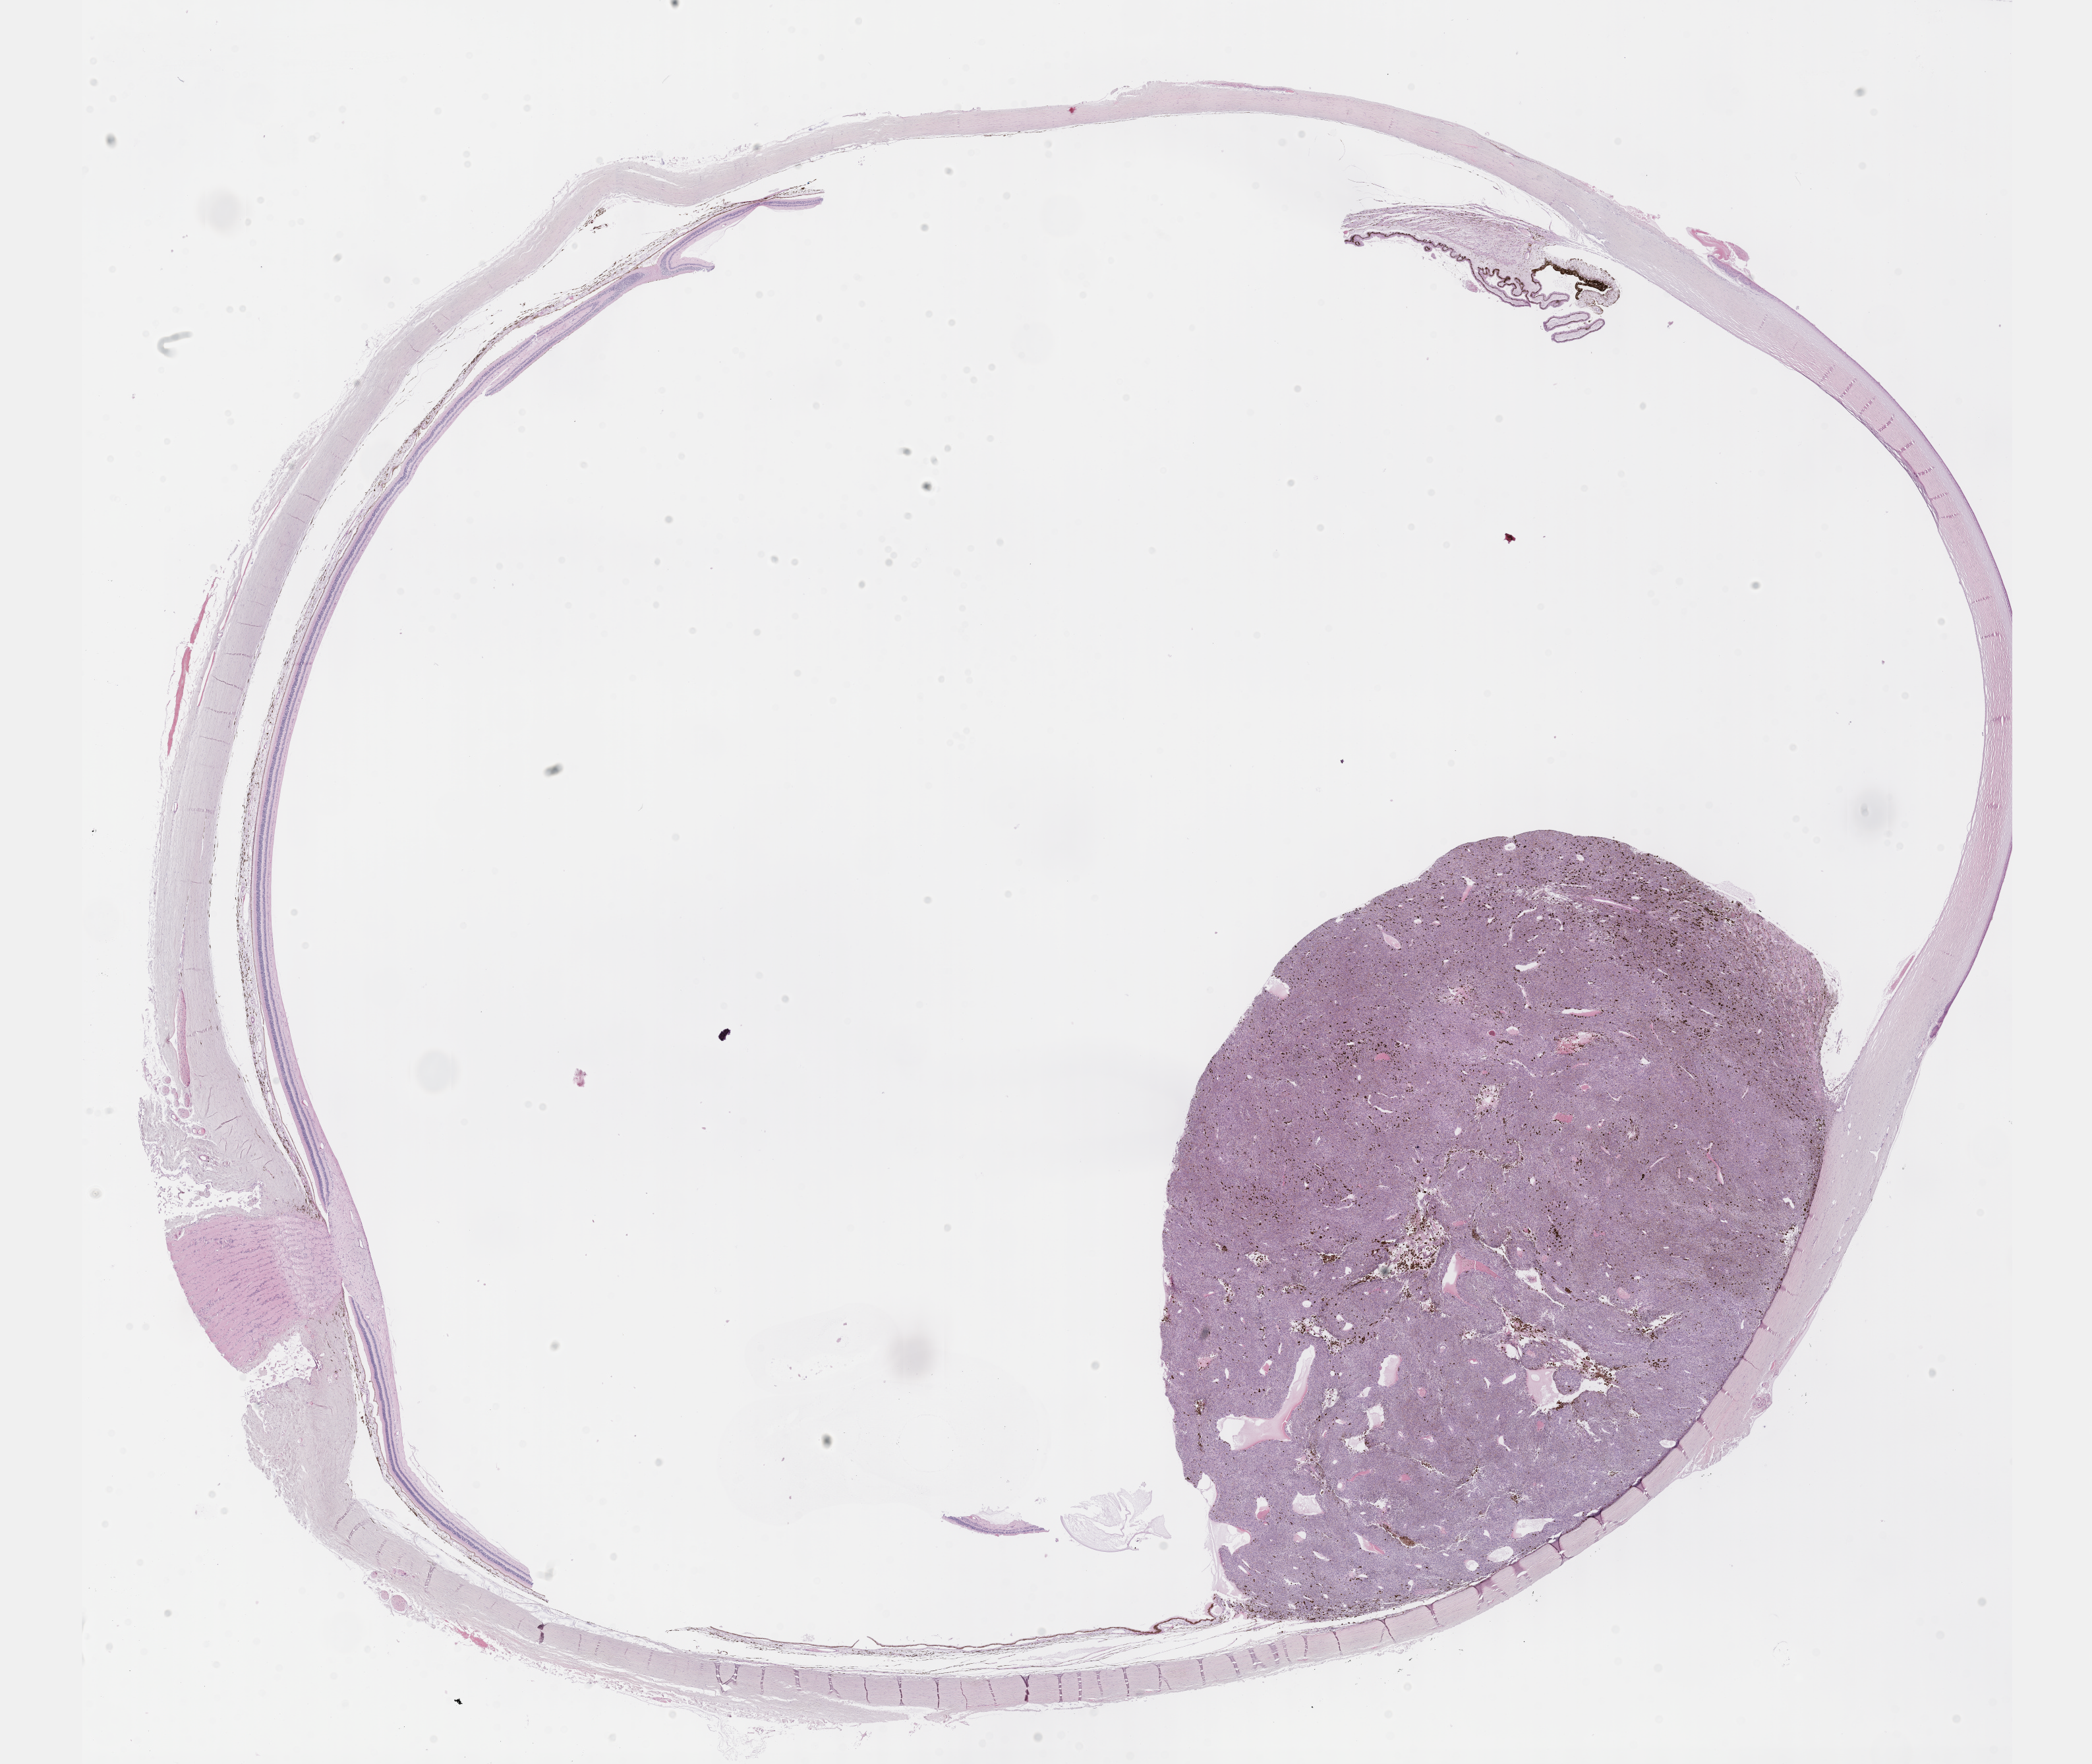
Whole-slide histology image, H&E — whole scanned area (about 25.7 x 21.6 mm, from a 40x scan) shown as a low-resolution overview; FFPE section; sample: primary tumour, uvea. Female patient; age at initial diagnosis 51 years.
TNM: T4b N0 M0. Diagnosis: Malignant melanoma, NOS. AJCC pathologic stage: IIIB.